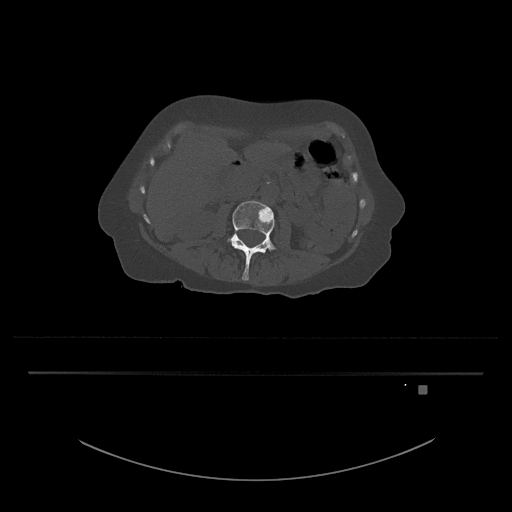
CT including the spine, one axial slice. Slice 427 of 797 in the series (ordered by position). Bone window (W 1800 / L 400 HU). 512 × 512 image matrix, field of view 500 × 500 mm. Patient: female, 57 years. From the clinical record (not read from this slice): primary cancer: cervical.
Annotated regions visible in this slice (semi-automatic segmentation, software-assisted and operator-edited):
- L3 vertebra: bounding box [x1, y1, x2, y2] px = [226, 201, 277, 281]